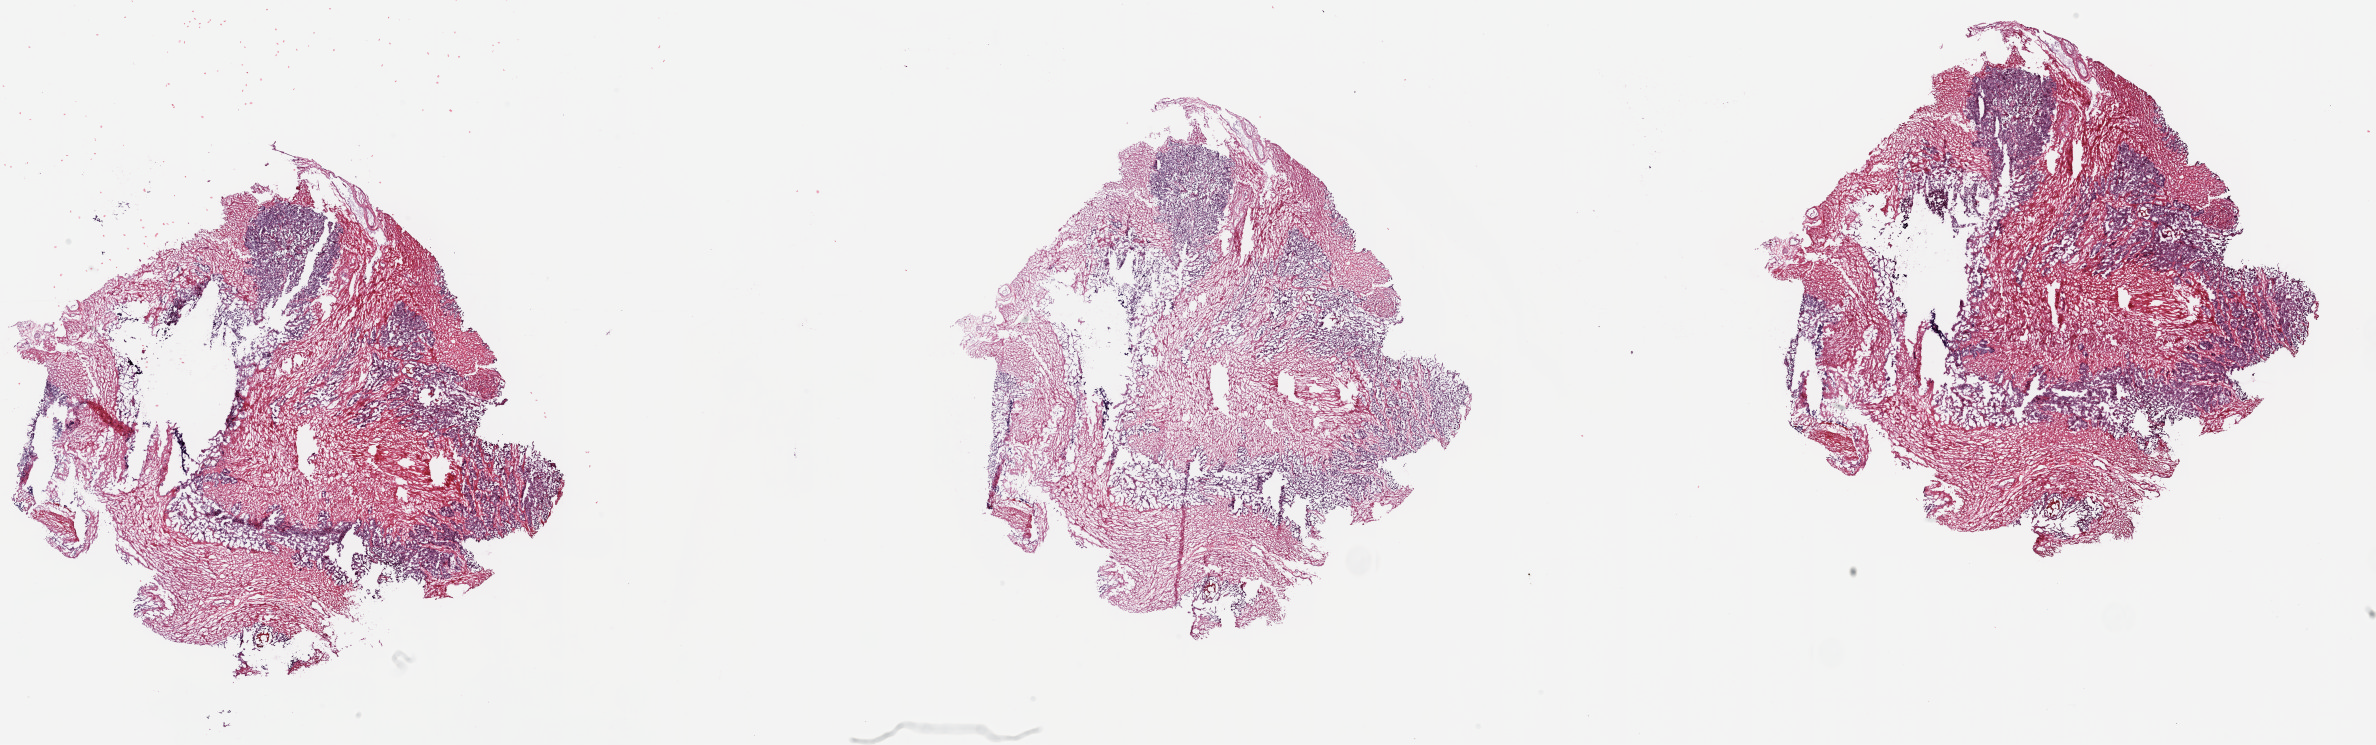
Whole-slide histology image, Hematoxylin and eosin (H&E) stained — a low-resolution overview of the entire scanned area, about 37.7 x 11.8 mm; frozen section; sample: solid tissue normal (non-tumour tissue), prostate. Male, age 62 years at initial diagnosis. Slide review estimates, as recorded: tumour cells 0%, tumour nuclei 0%, normal cells 30%, stromal cells 70%, necrosis 0%. Inflammatory infiltration, as recorded: lymphocyte infiltration 3%, monocyte infiltration 0%, neutrophil infiltration 0%.
- this section: solid tissue normal (non-tumour) sample from the same patient
- patient diagnosis: Adenocarcinoma, NOS (prostate gland)